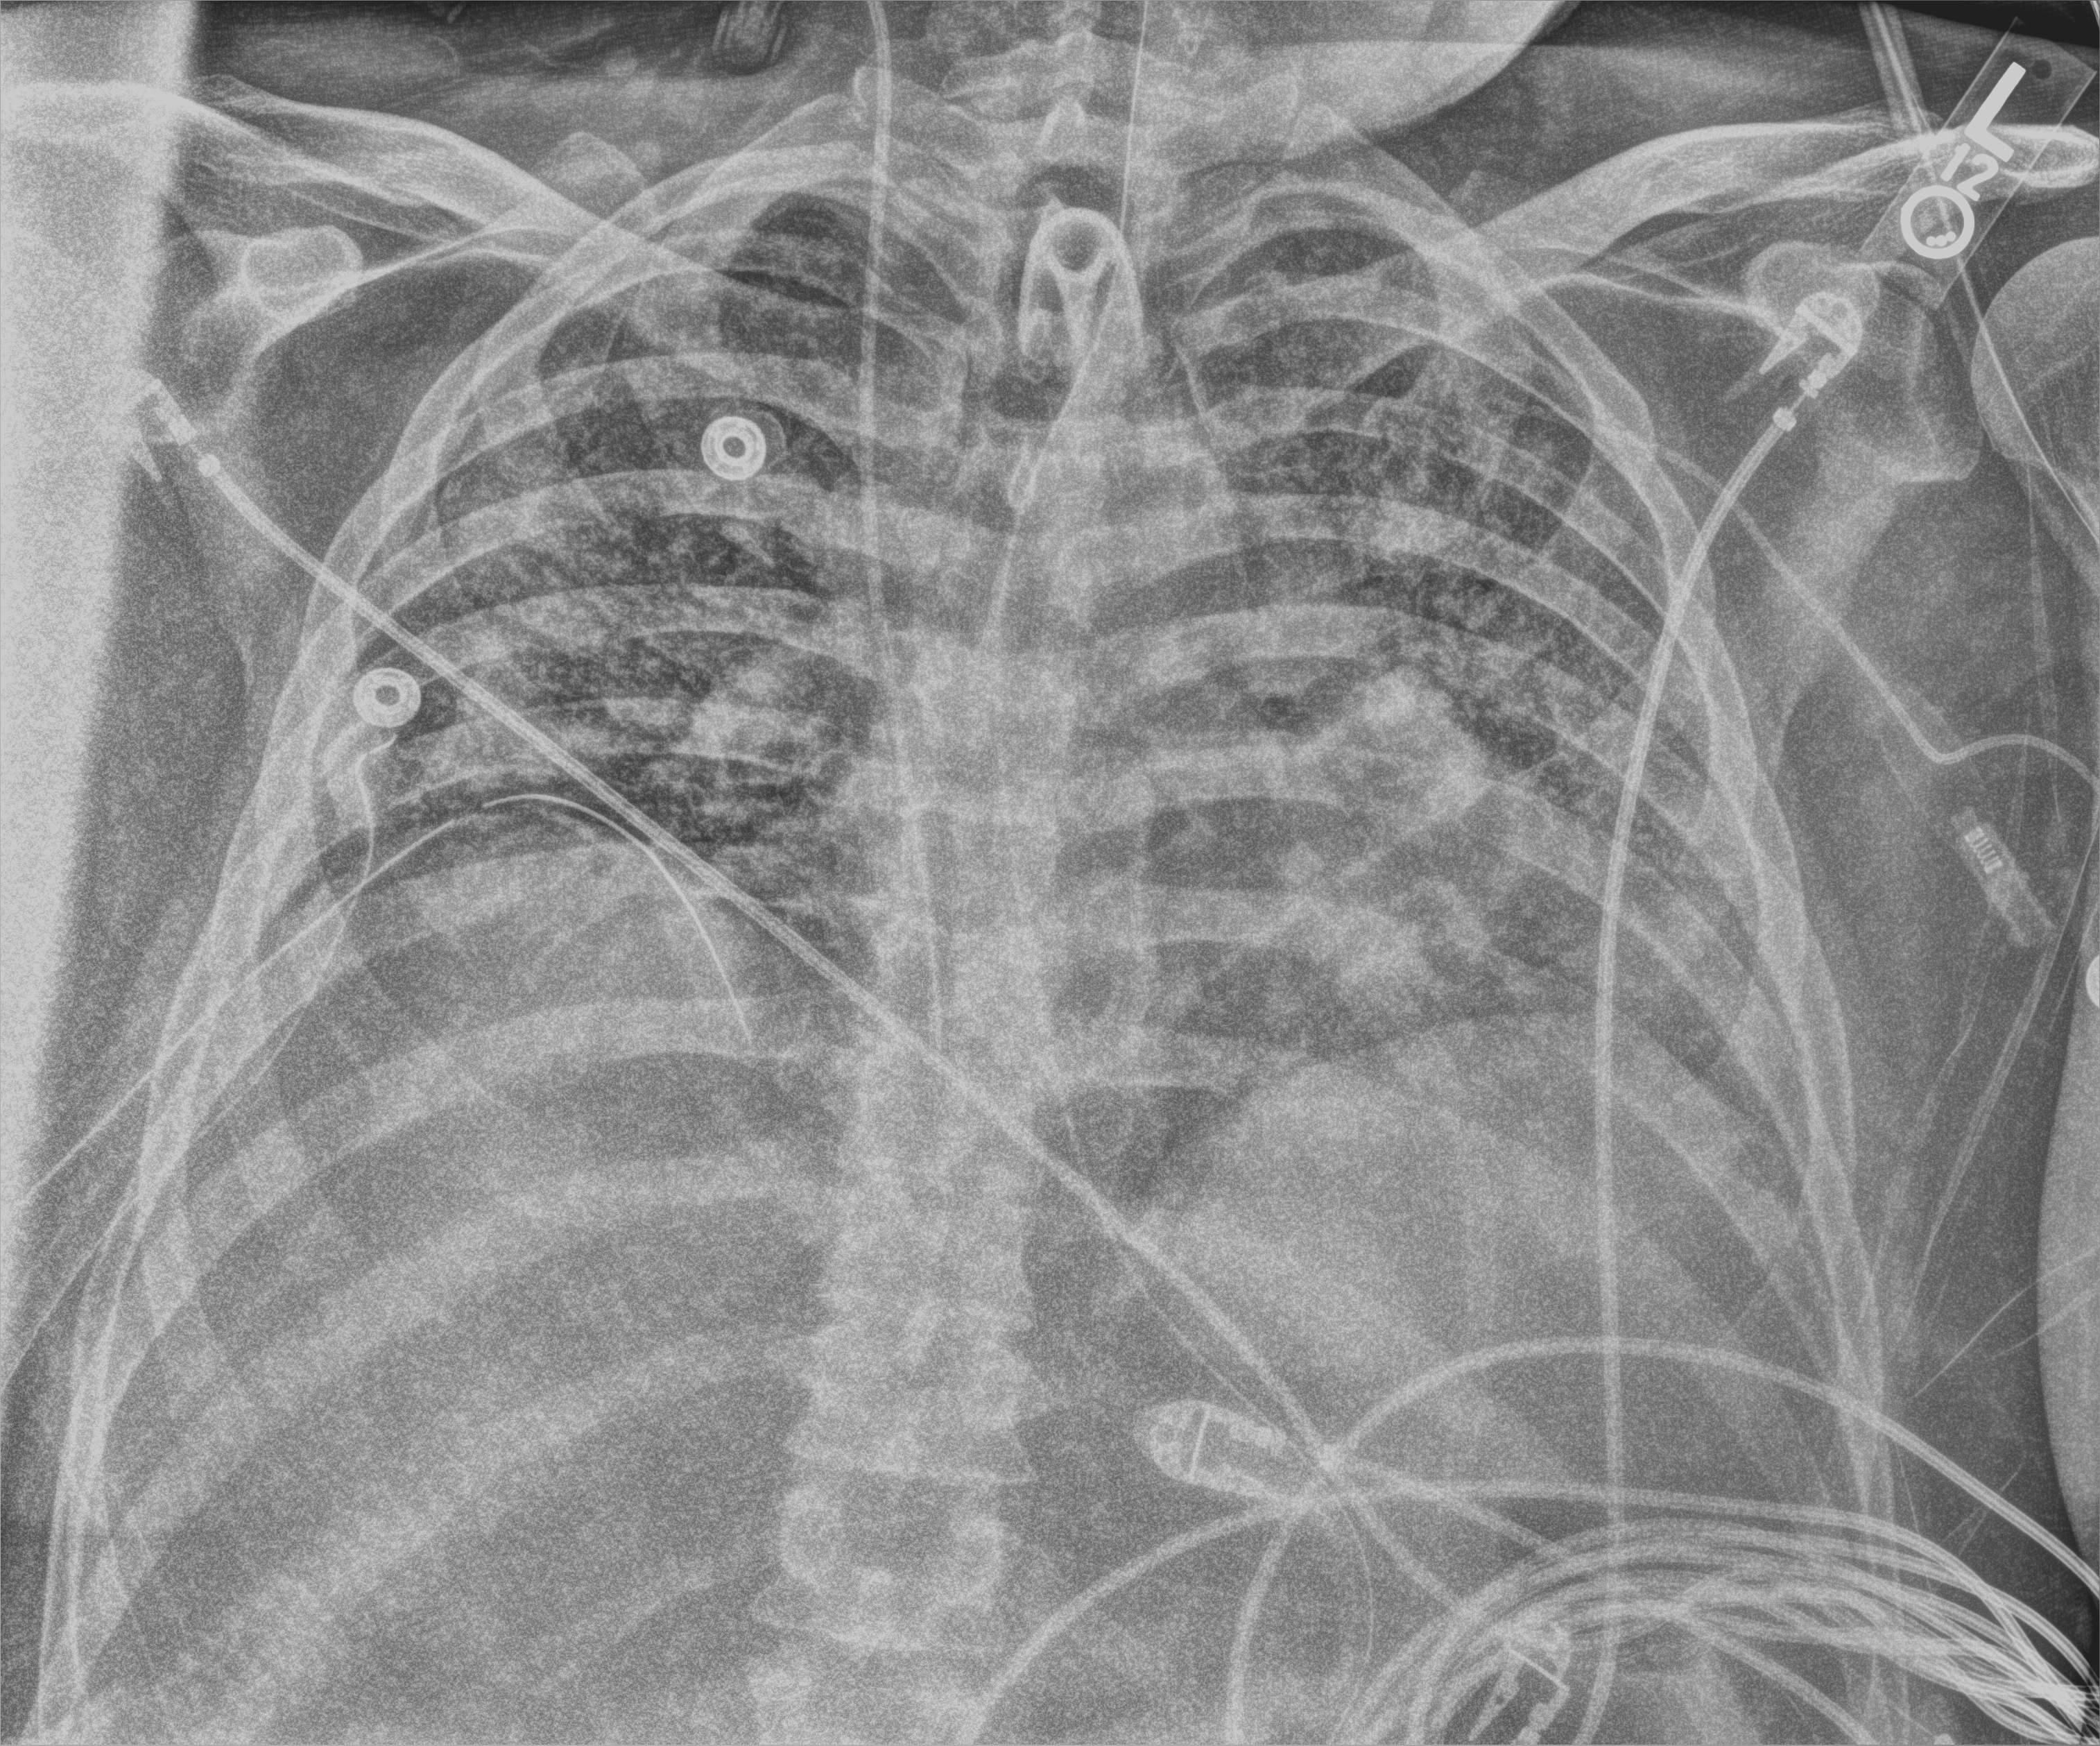
Portable chest radiograph, anteroposterior (AP) projection. Patient hospitalised with COVID-19; male, aged 18–59 years.
Hospital-stay facts (about this admission, not read from this image; timing relative to this image not recorded): length of hospital stay: 80 days; admitted to intensive care during this hospital stay: yes; mechanically ventilated during this hospital stay: yes.